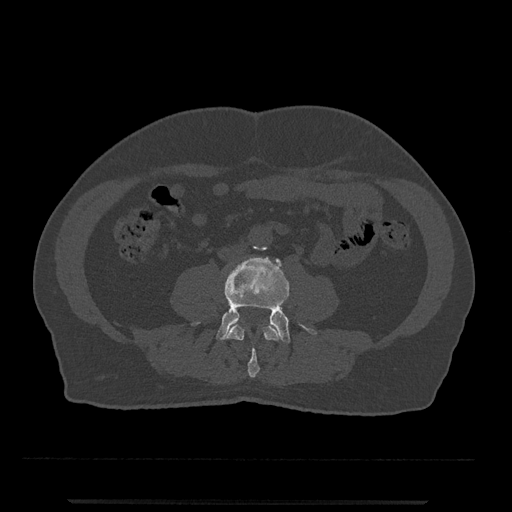
CT including the spine, one axial slice. Slice 162 of 797 in the series (ordered by position). Reconstruction kernel Br40s/3. 120 kVp. Bone window (W 1800 / L 400 HU). 512 × 512 image matrix, field of view 419 × 419 mm. Patient: male, 63 years. Case-level facts recorded for this patient, not image findings: primary cancer: prostate.
Annotated regions visible in this slice (semi-automatic segmentation, software-assisted and operator-edited):
- L3 vertebra: box from (x=226, y=324) to (x=280, y=378) px
- L4 vertebra: (x=195, y=257)–(x=317, y=343)